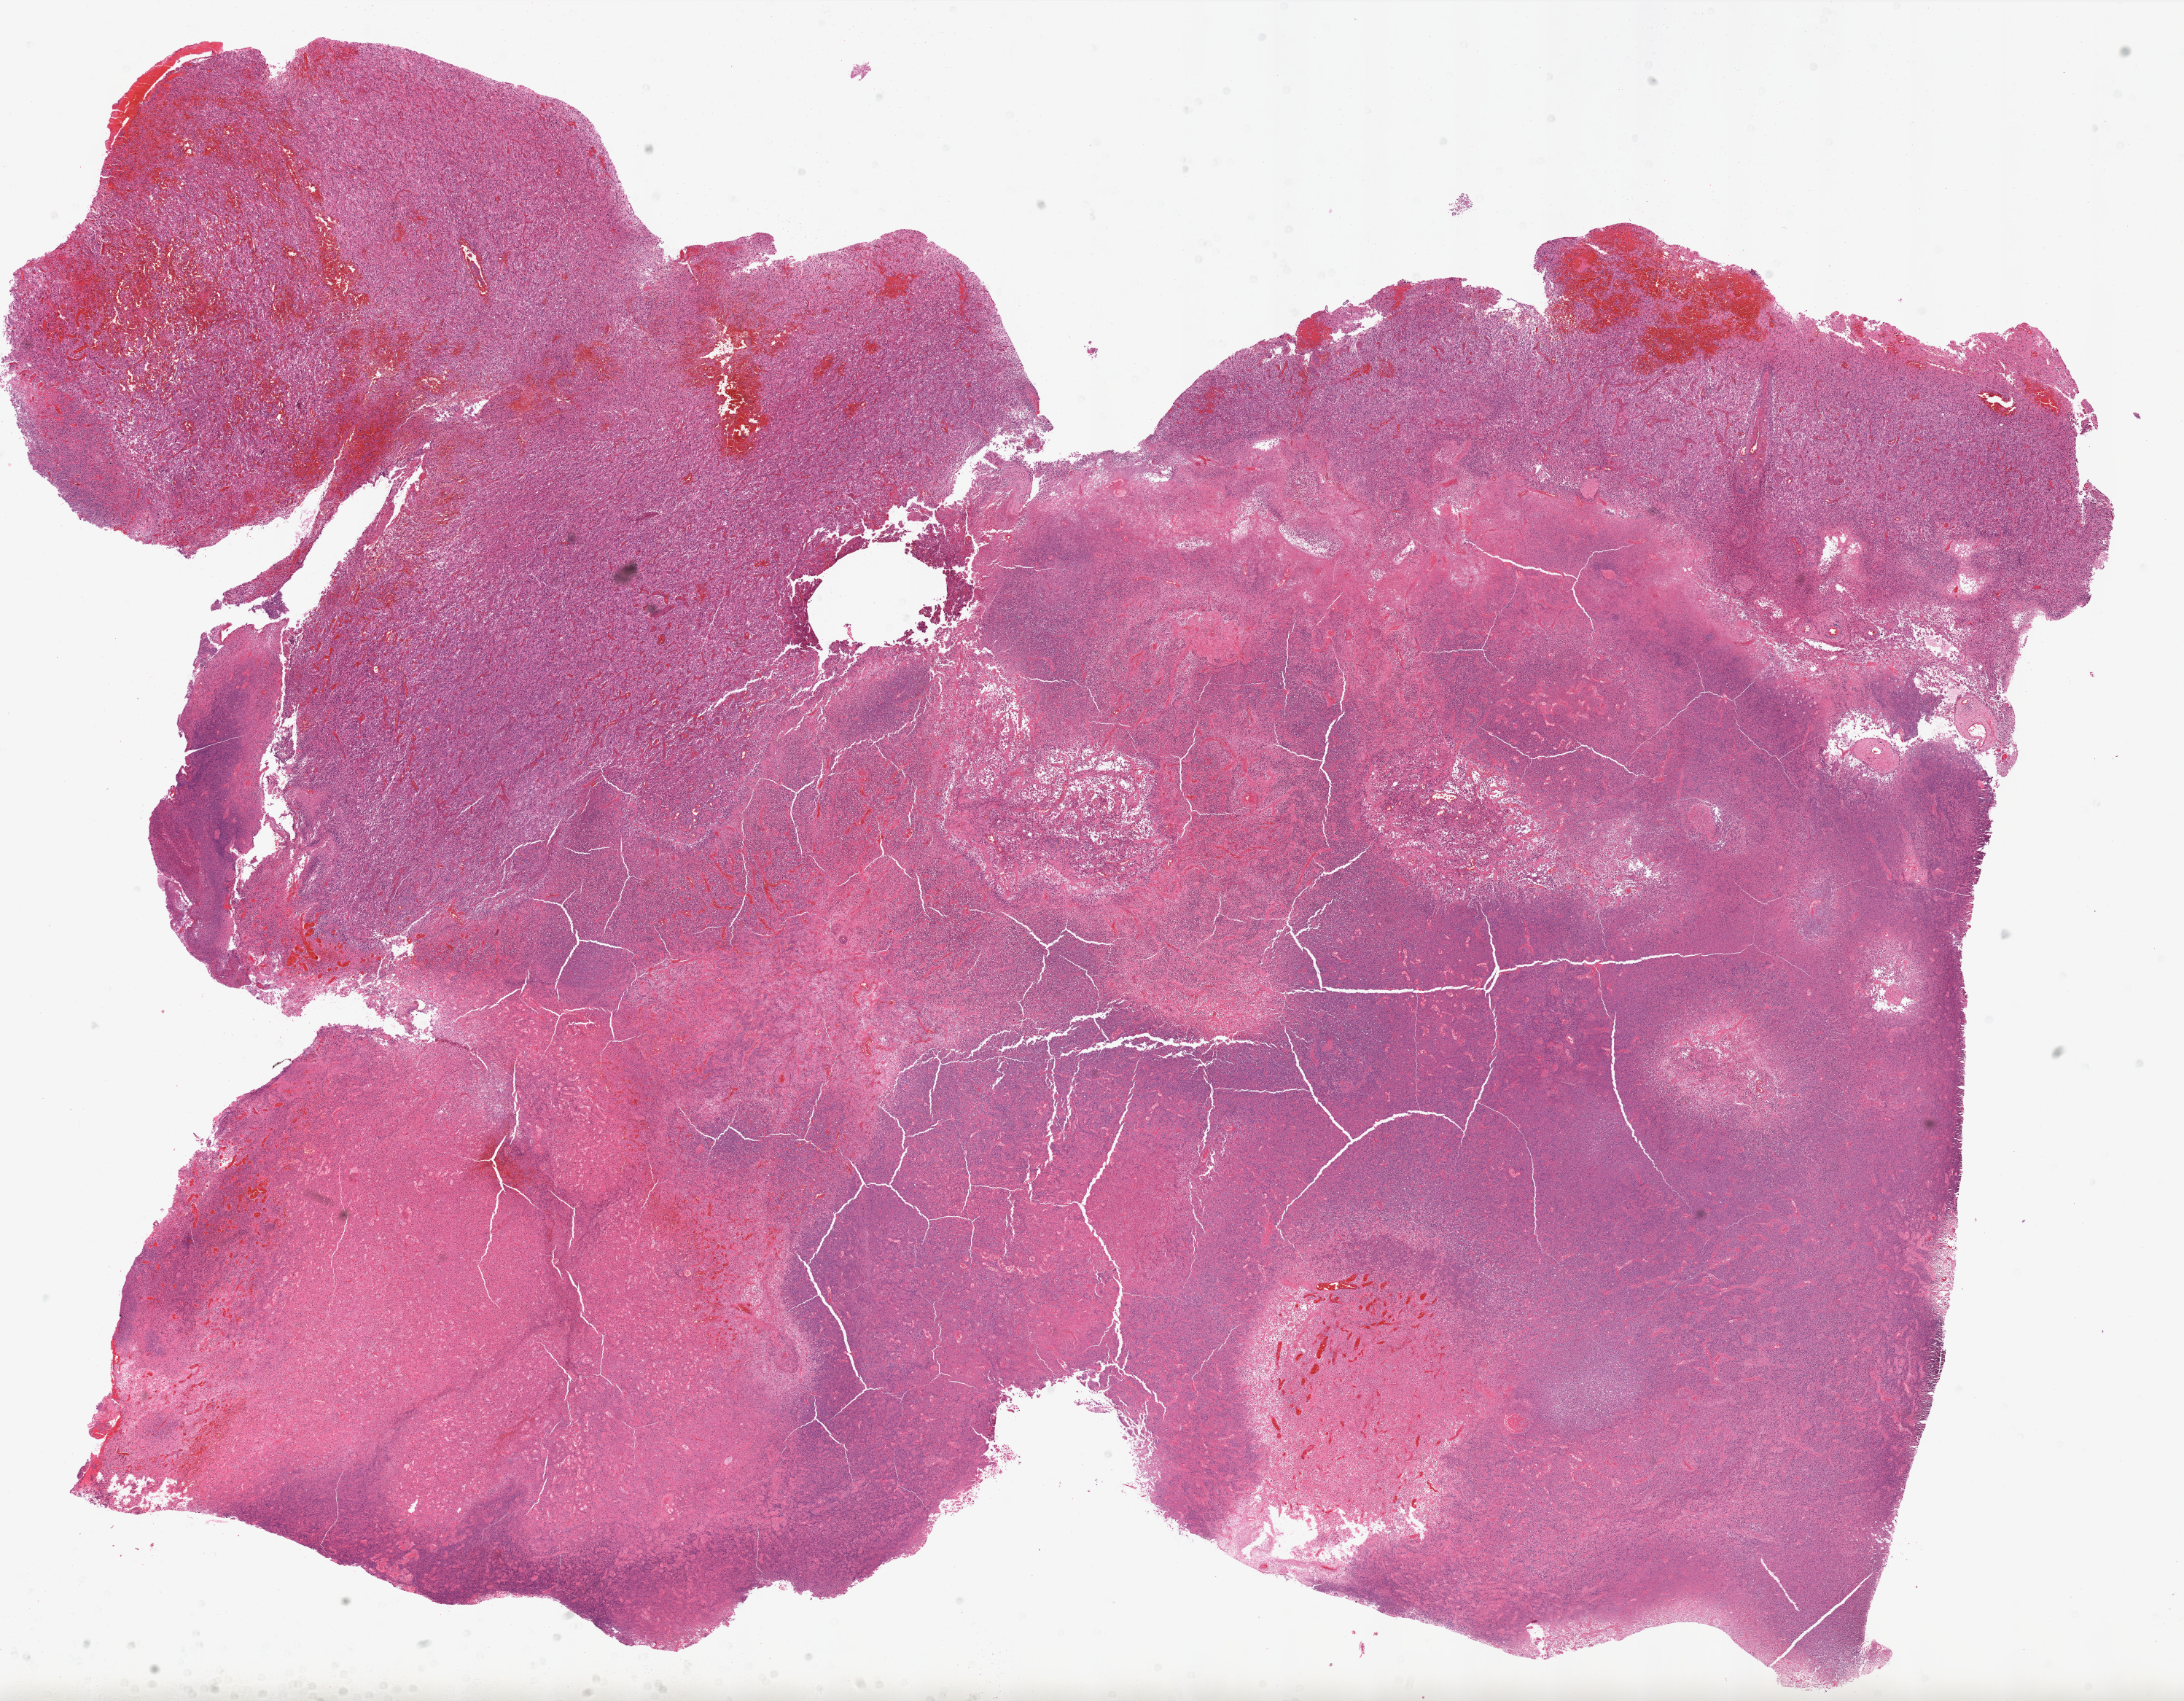
H&E whole-slide image, whole scanned area (about 24.0 x 18.7 mm, slide scanned at 20x) shown as a low-resolution overview; formalin-fixed paraffin-embedded (FFPE) diagnostic section; brain, primary tumour sample. Female patient; age at initial diagnosis 52 years.
Diagnosis: Glioblastoma.